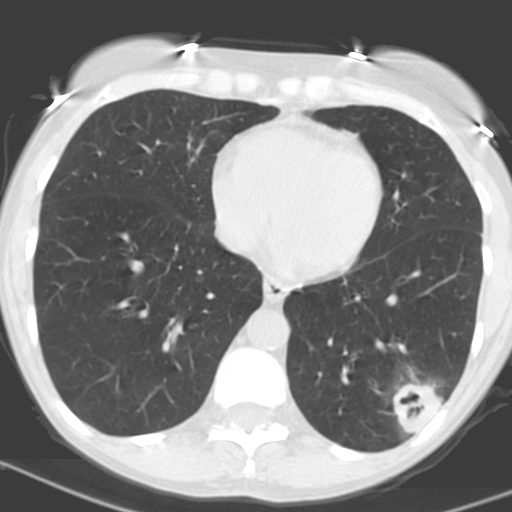
Low-dose screening chest CT, one axial slice; position 57 of 156 along the scan axis; lung window (W 1500 / L -600 HU); 3.2 mm slice thickness; 512 × 512 image matrix.
Annotated regions visible in this slice (outlined manually by an expert reader):
- lesion 1 (tumor, lower lobe of left lung): bounding box [x1, y1, x2, y2] px = [393, 379, 443, 435]